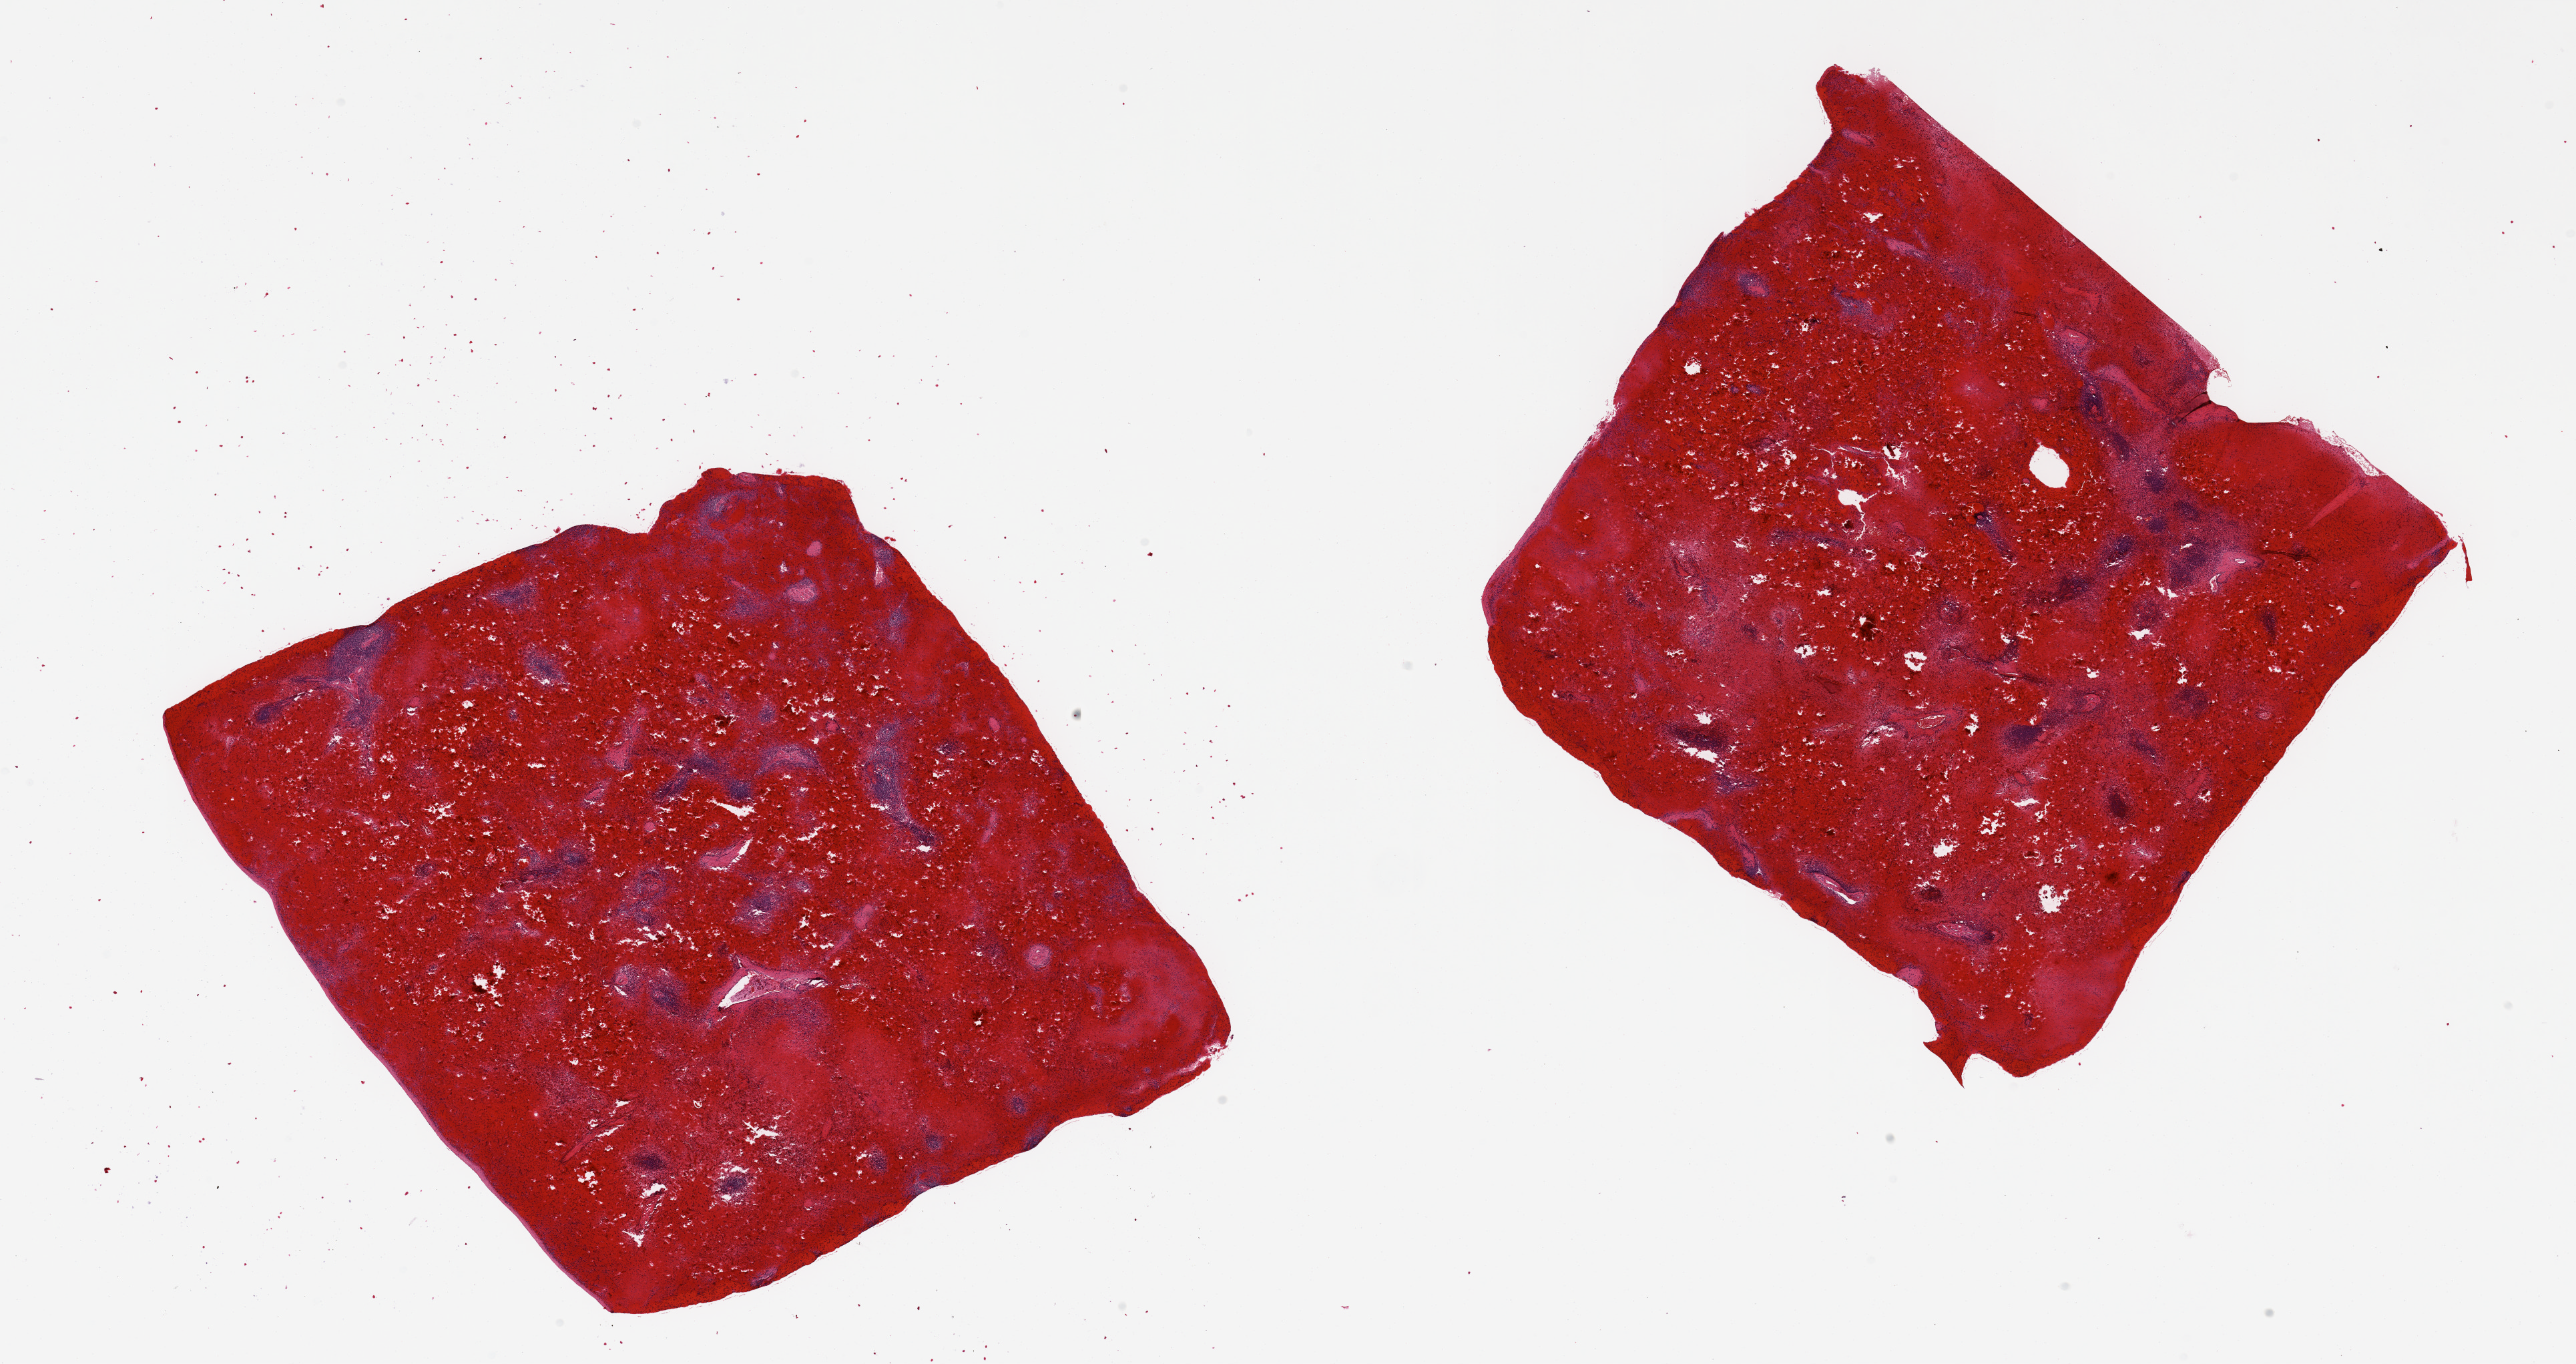
H&E whole-slide image, brightfield — low-resolution overview of the scanned area, about 30.5 x 16.2 mm (from a 20x scan); PAXgene-fixed, paraffin-embedded tissue; section of spleen (target tissue); tissue donor sample. Donor: female.
Reviewer comment on this tissue sample: 2 pieces; severe congestion.